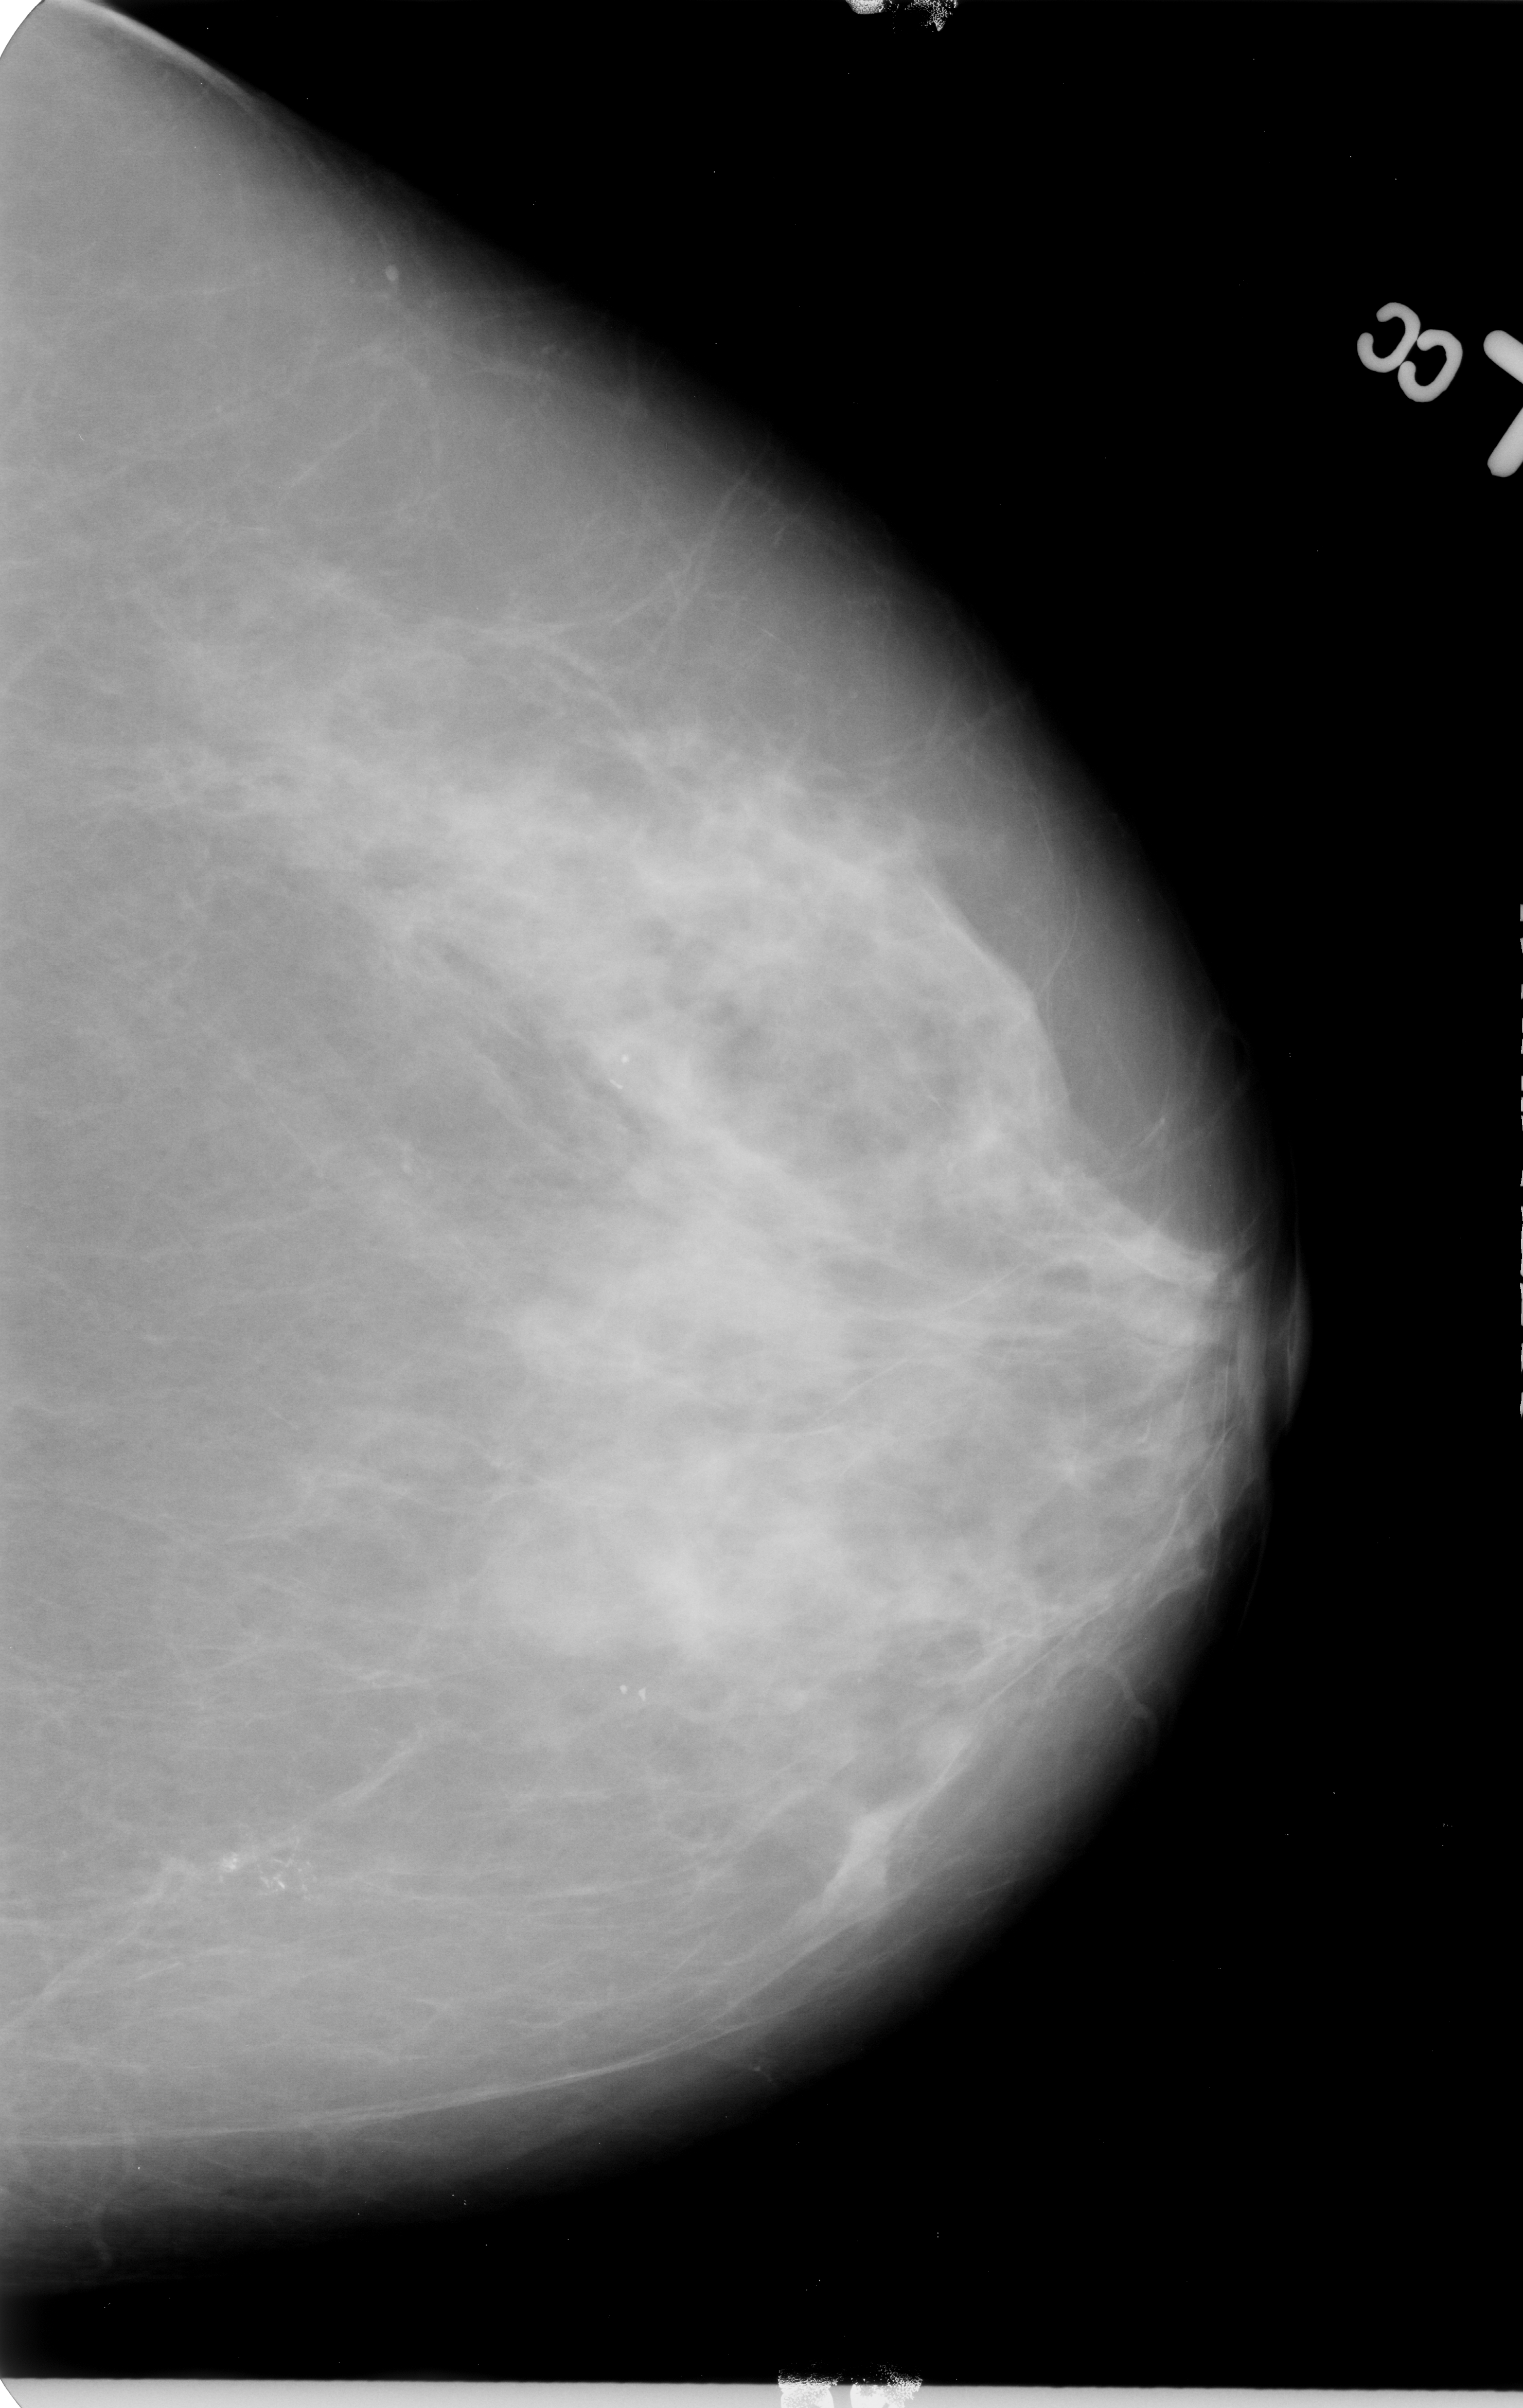
Scanned film-screen mammogram; left breast; CC view; breast composition: heterogeneously dense (BI-RADS density category 3 of 4).
Marked findings (only marked abnormalities are described; nothing is implied about the rest of the image): calcifications, morphology pleomorphic / fine linear branching, distribution clustered / linear; BI-RADS assessment category 5; subtlety rating 4 on a 1 (subtle) to 5 (obvious) scale; pathology (as recorded): malignant.